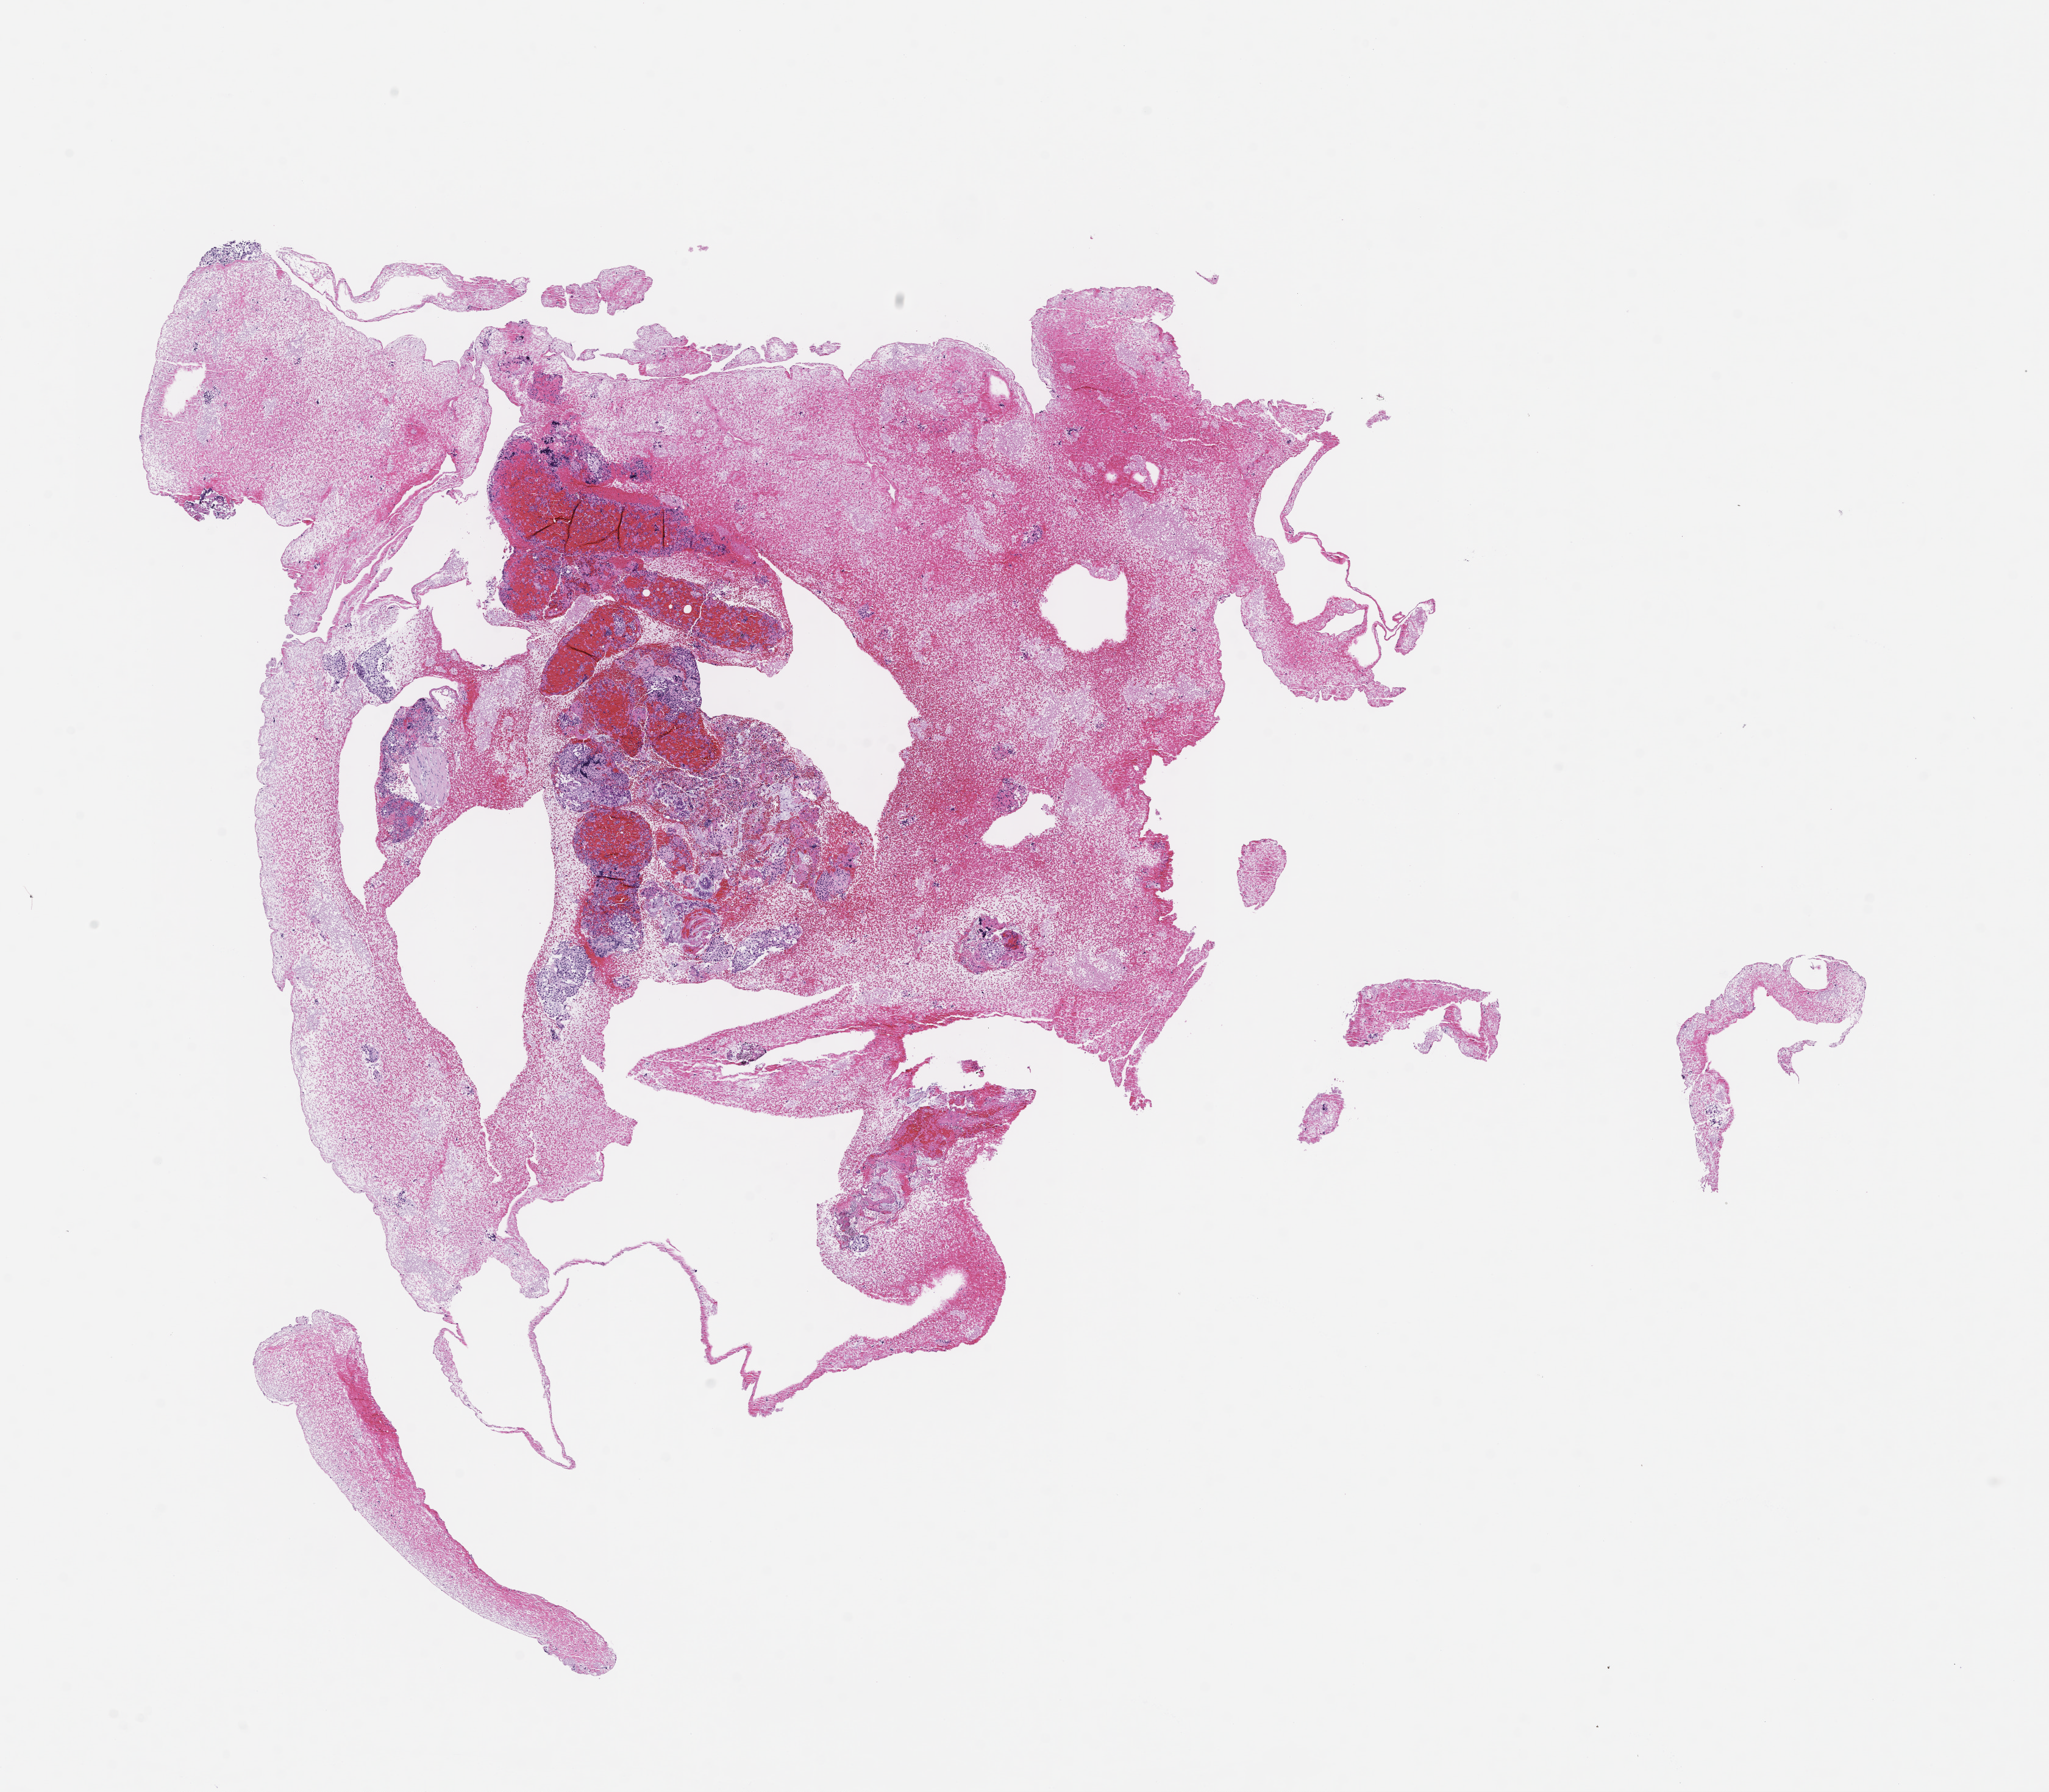
Whole-slide image, hematoxylin and eosin (H&E) stain, whole scanned area (about 13.6 x 11.9 mm) shown as a low-resolution overview. Formalin-fixed paraffin-embedded section. Archival tissue. Male patient.
This section: metastasis (sampled organ not recorded). Primary diagnosis of the patient: Non-Small Cell Lung Carcinoma.